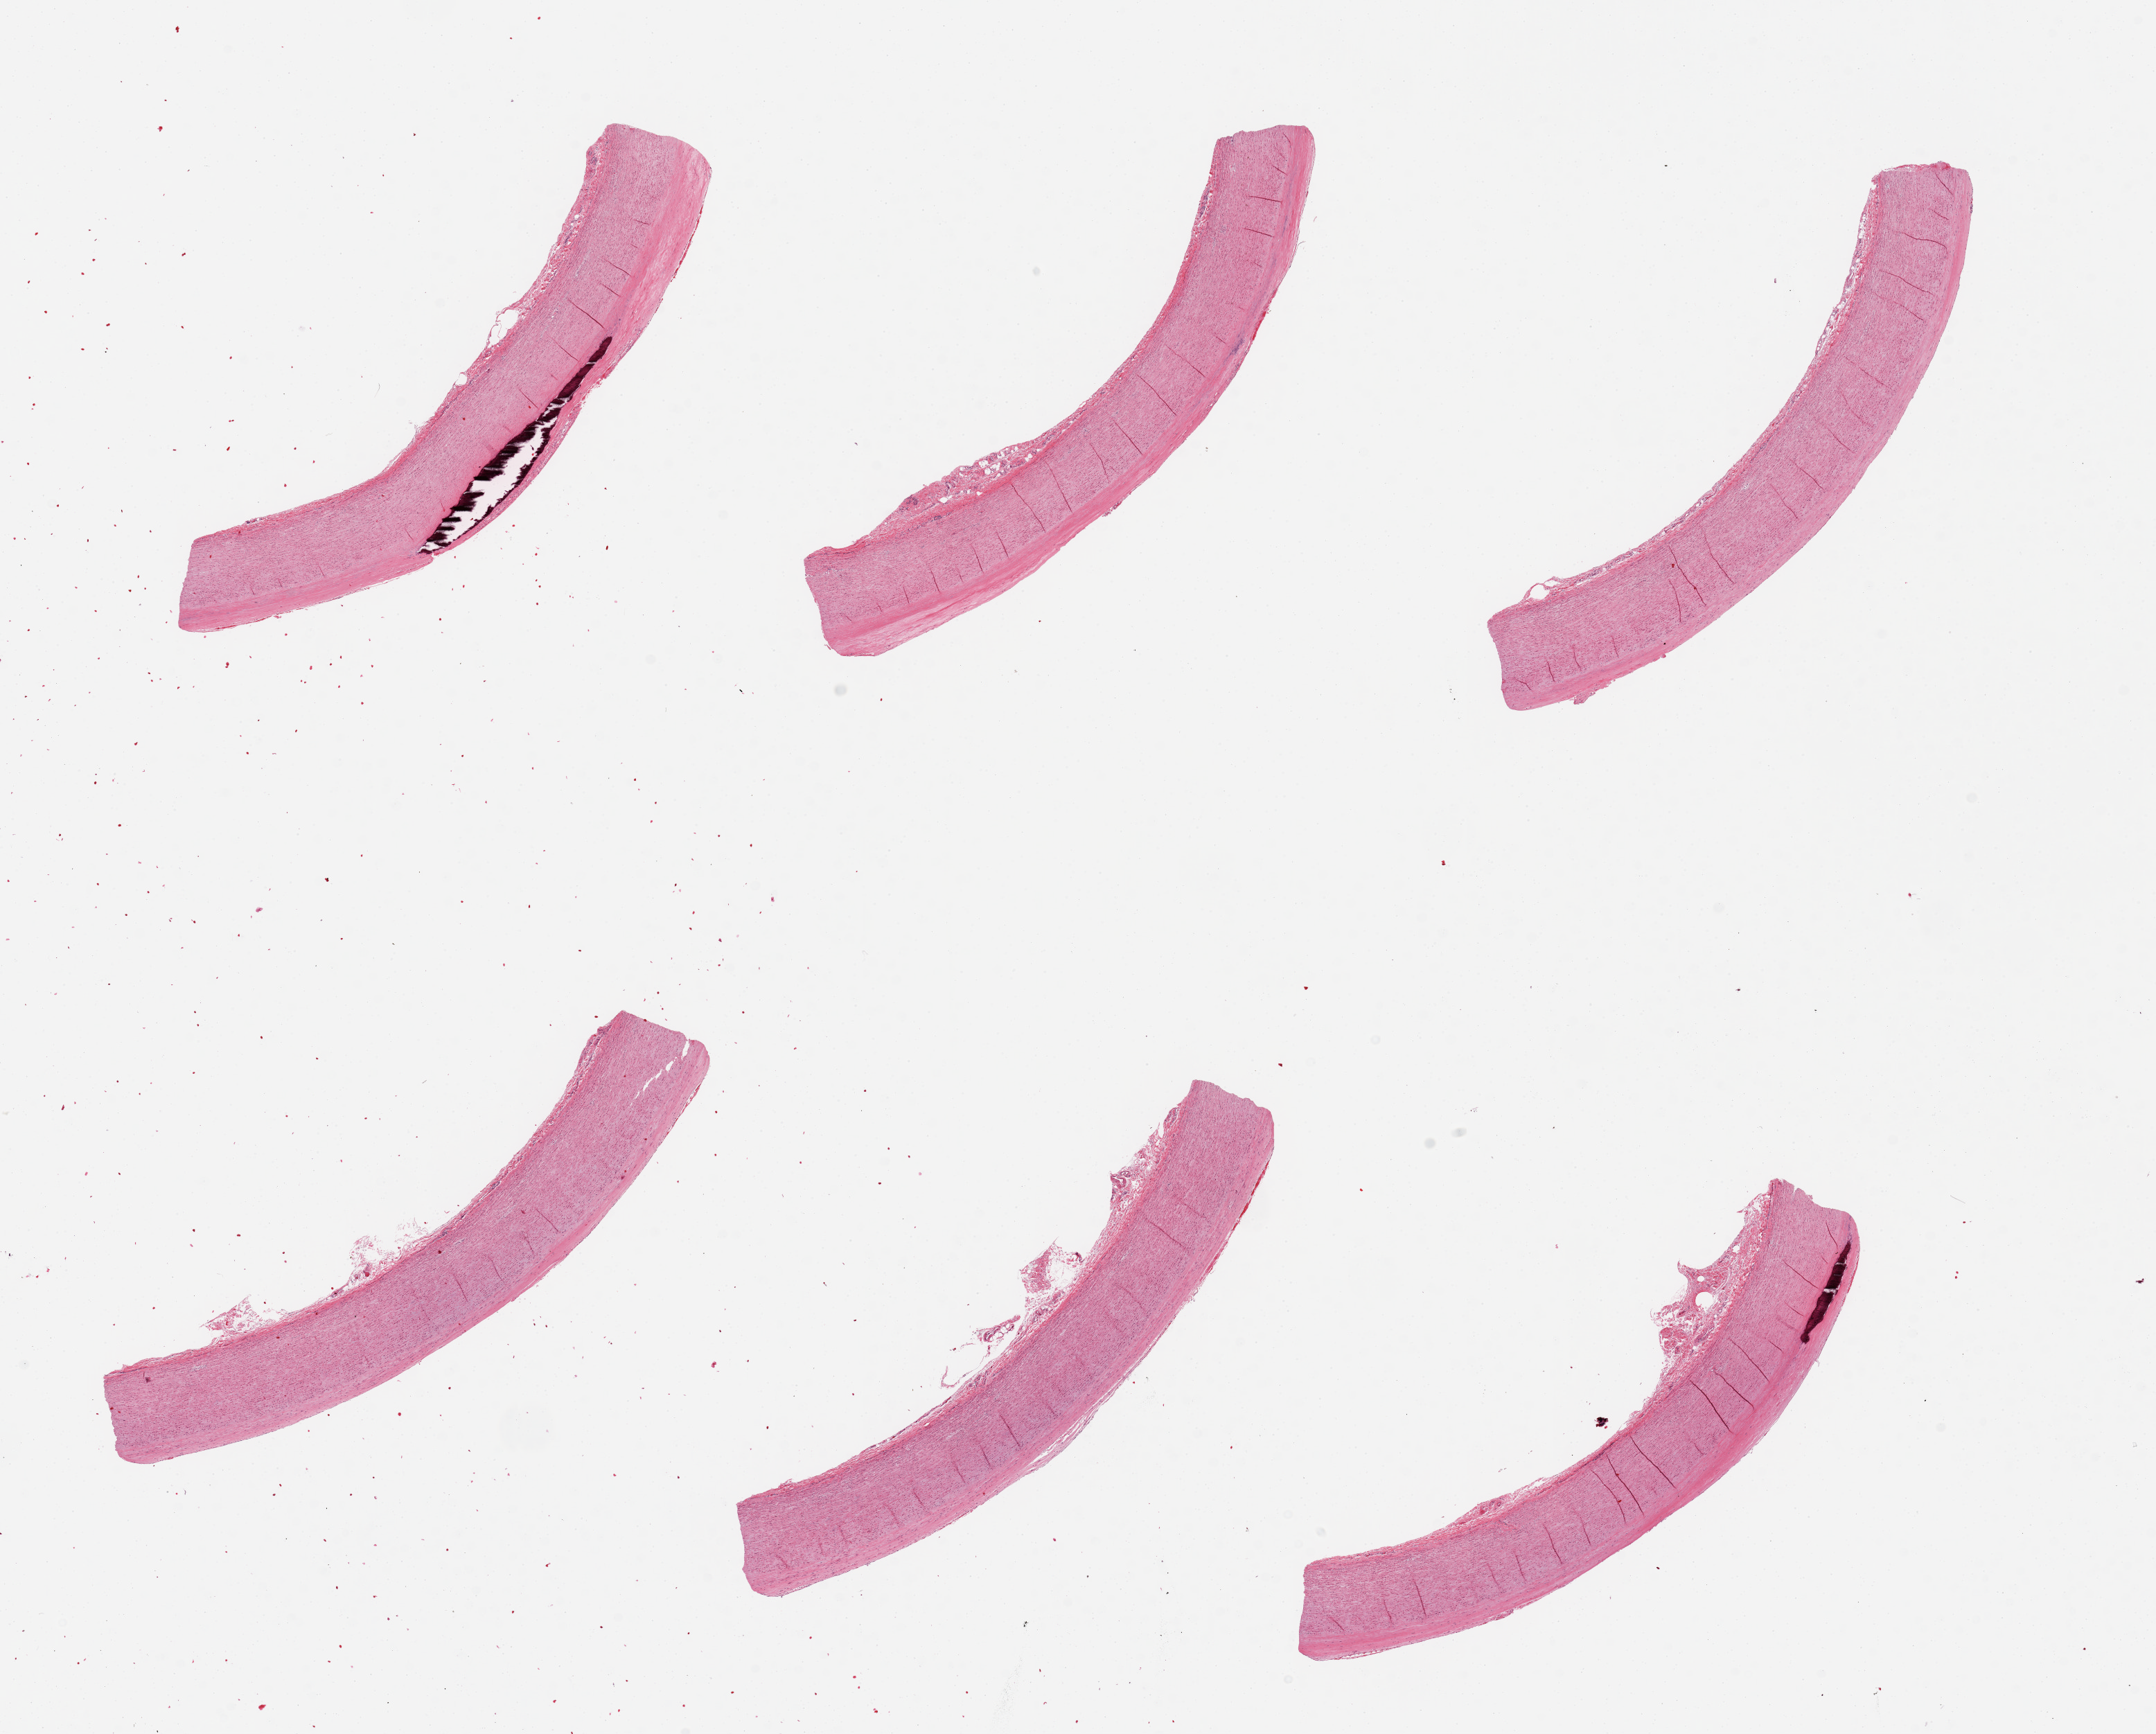
Hematoxylin and eosin (H&E) whole-slide image, shown as a low-resolution overview of the whole scanned area (about 24.6 x 19.8 mm, slide scanned at 20x). Female donor.
Specimen: PAXgene-fixed paraffin-embedded (PFPE) section; sampled site (target tissue): aorta; donor tissue sample.